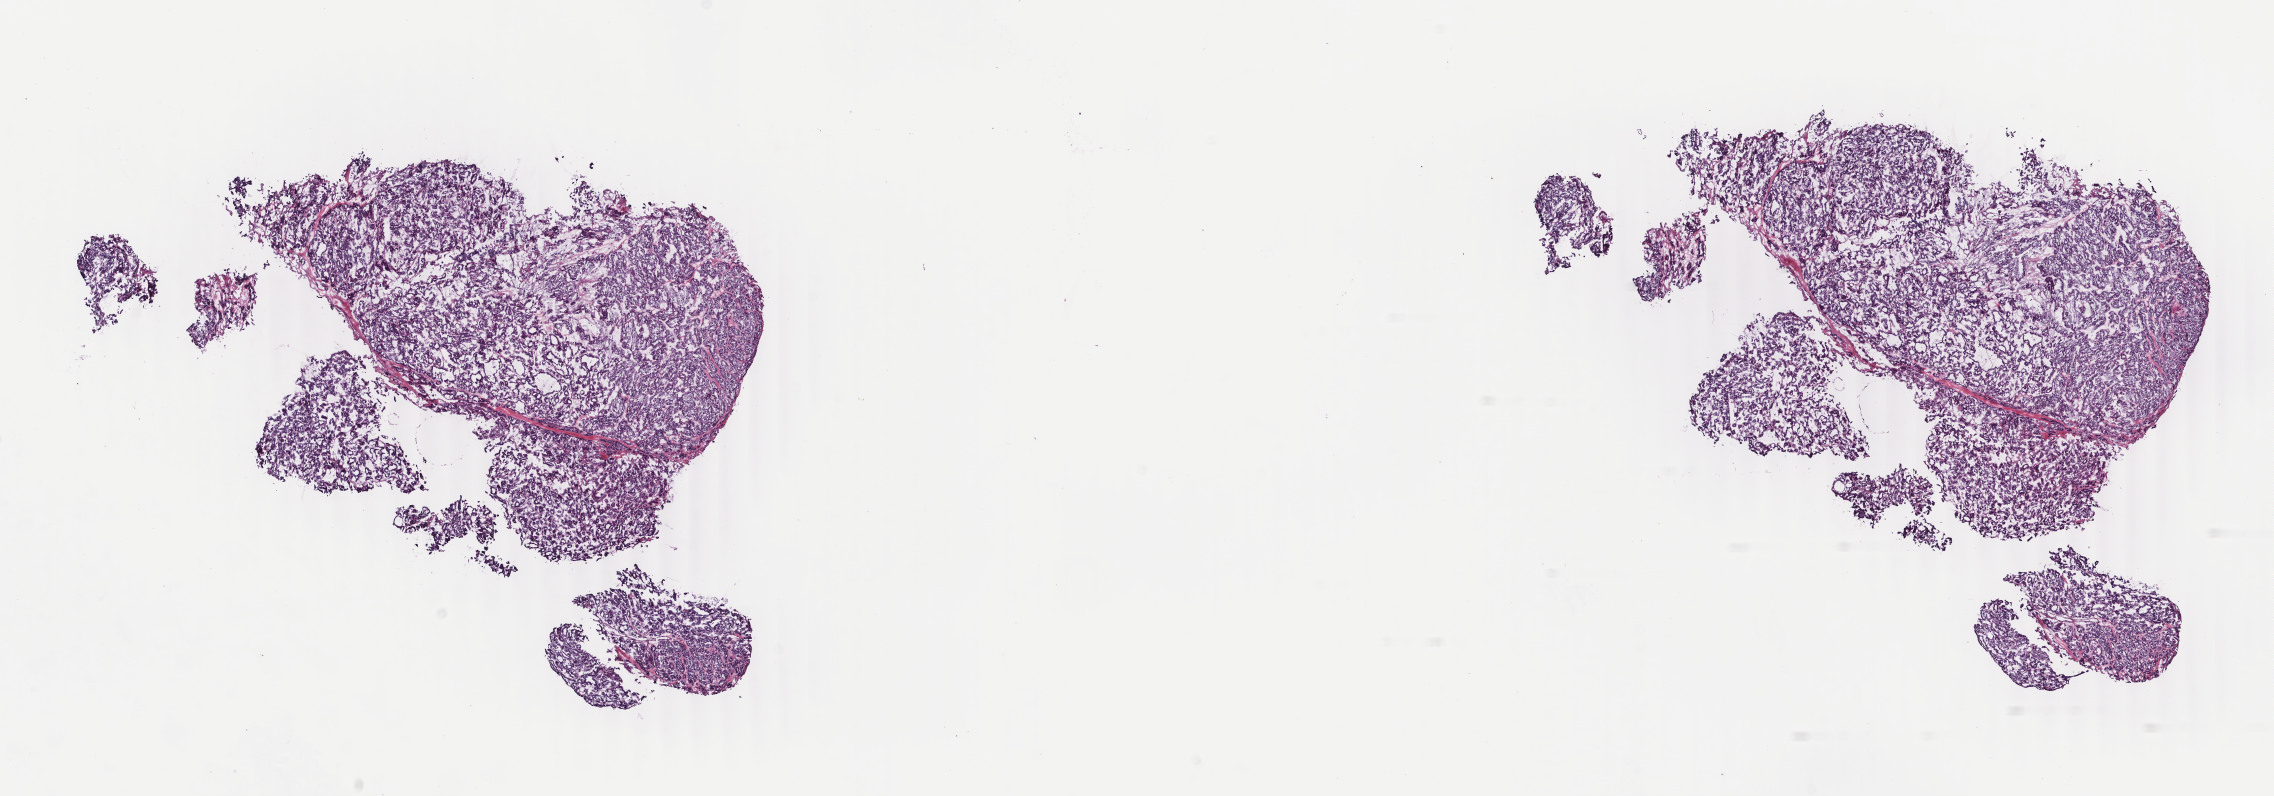
Whole-slide histology image, H&E-stained, whole scanned area (about 18.1 x 6.3 mm) shown as a low-resolution overview, frozen section from the top of the tissue portion, thyroid, primary tumour sample. Female patient; age at initial diagnosis 46 years. Pathologist review of this section (percent, as recorded): tumour cells 100%, tumour nuclei 85%, normal cells 0%, stromal cells 0%, necrosis 0%. Inflammatory infiltration, as recorded: lymphocyte infiltration 0%, monocyte infiltration 0%, neutrophil infiltration 0%.
Laterality: left. Lymph nodes positive (case pathology): 10 of 83 examined. Histologic diagnosis: Papillary adenocarcinoma, NOS (thyroid gland). AJCC pathologic stage: IVA (7th edition).